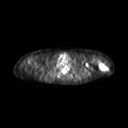
FDG PET of an extremity soft-tissue mass (from a PET/CT study), one axial slice. Position 204 of 267 along the scan axis. 128 × 128 image matrix, field of view 600 × 600 mm. Patient: female, 28 years. Case-level facts recorded for this patient, not image findings: histological type: malignant fibrous histiocytoma; grade: low; site of the primary tumour: left arm.
Annotated regions visible in this slice (expert contour drawn on MRI and transferred to this co-registered scan by the dataset authors):
- gross tumour volume (mass): bounding box (x1, y1, x2, y2) in pixels: (98, 62, 106, 70)